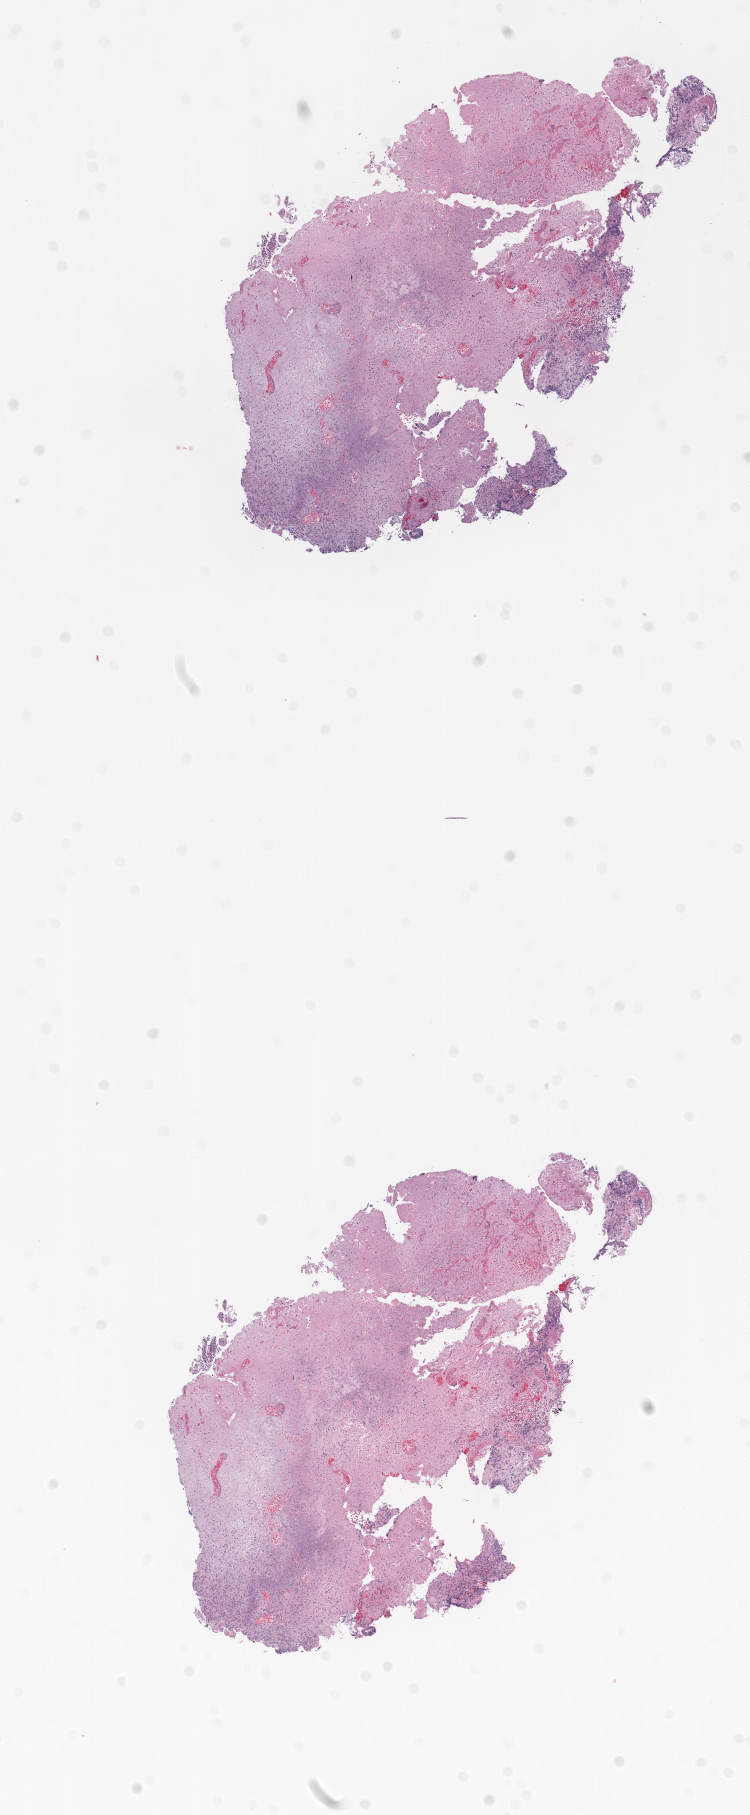
Digitized H&E tissue section (whole slide), shown as a low-resolution overview of the whole scanned area (about 6.0 x 14.6 mm, slide scanned at 20x); formalin-fixed paraffin-embedded (FFPE) diagnostic section; brain, primary tumour sample. Male patient; age at initial diagnosis 50 years.
Histologic diagnosis: Glioblastoma.